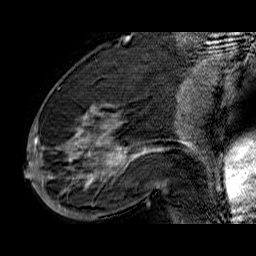
Breast MRI (dynamic contrast-enhanced), one sagittal slice; slice 24 of 60 in the series (ordered by position); dynamic contrast-enhanced series, time point 2 of 6 at this slice position (early post-contrast); 1.5 T; TE 6.5 ms, TR 32.9 ms; 4 mm slice thickness; 256 × 256 image matrix, field of view 200 × 200 mm. Female patient. From the clinical record (not read from this slice): setting: breast cancer imaged before/during neoadjuvant chemotherapy; receptor status: HR-positive, HER2-negative.
Annotated regions visible in this slice (semi-automatically segmented with operator editing):
- analysis volume of interest (the breast-tissue region the enhancement analysis was run in; not a lesion): bounding box (x1, y1, x2, y2) in pixels: (33, 74, 176, 210)
- tumour enhancement mask (voxels above the 100 % enhancement threshold inside the analysis volume of interest): (33, 106, 148, 197)